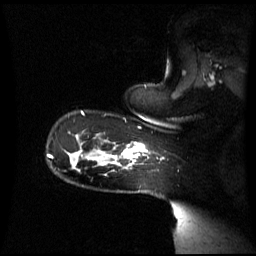
Breast MRI (dynamic contrast-enhanced), one sagittal slice. Slice 48 of 60 in the series (ordered by position). Dynamic contrast-enhanced series, image 2 of 3 at this slice position (ordered by acquisition). 1.5 T. TE 4.2 ms, TR 8.4 ms. 2.8 mm slice thickness. 256 × 256 image matrix, field of view 270 × 270 mm. Patient: female, 39 years. Case-level facts recorded for this patient, not image findings: setting: breast cancer imaged before/during neoadjuvant chemotherapy; receptor status: triple-negative.
Structures marked on this image (semi-automatically segmented with operator editing):
- analysis volume of interest (the breast-tissue region the enhancement analysis was run in; not a lesion): box from (x=101, y=143) to (x=149, y=171) px
- tumour enhancement mask (voxels above the 70 % enhancement threshold inside the analysis volume of interest): (x=103, y=143)–(x=147, y=165)